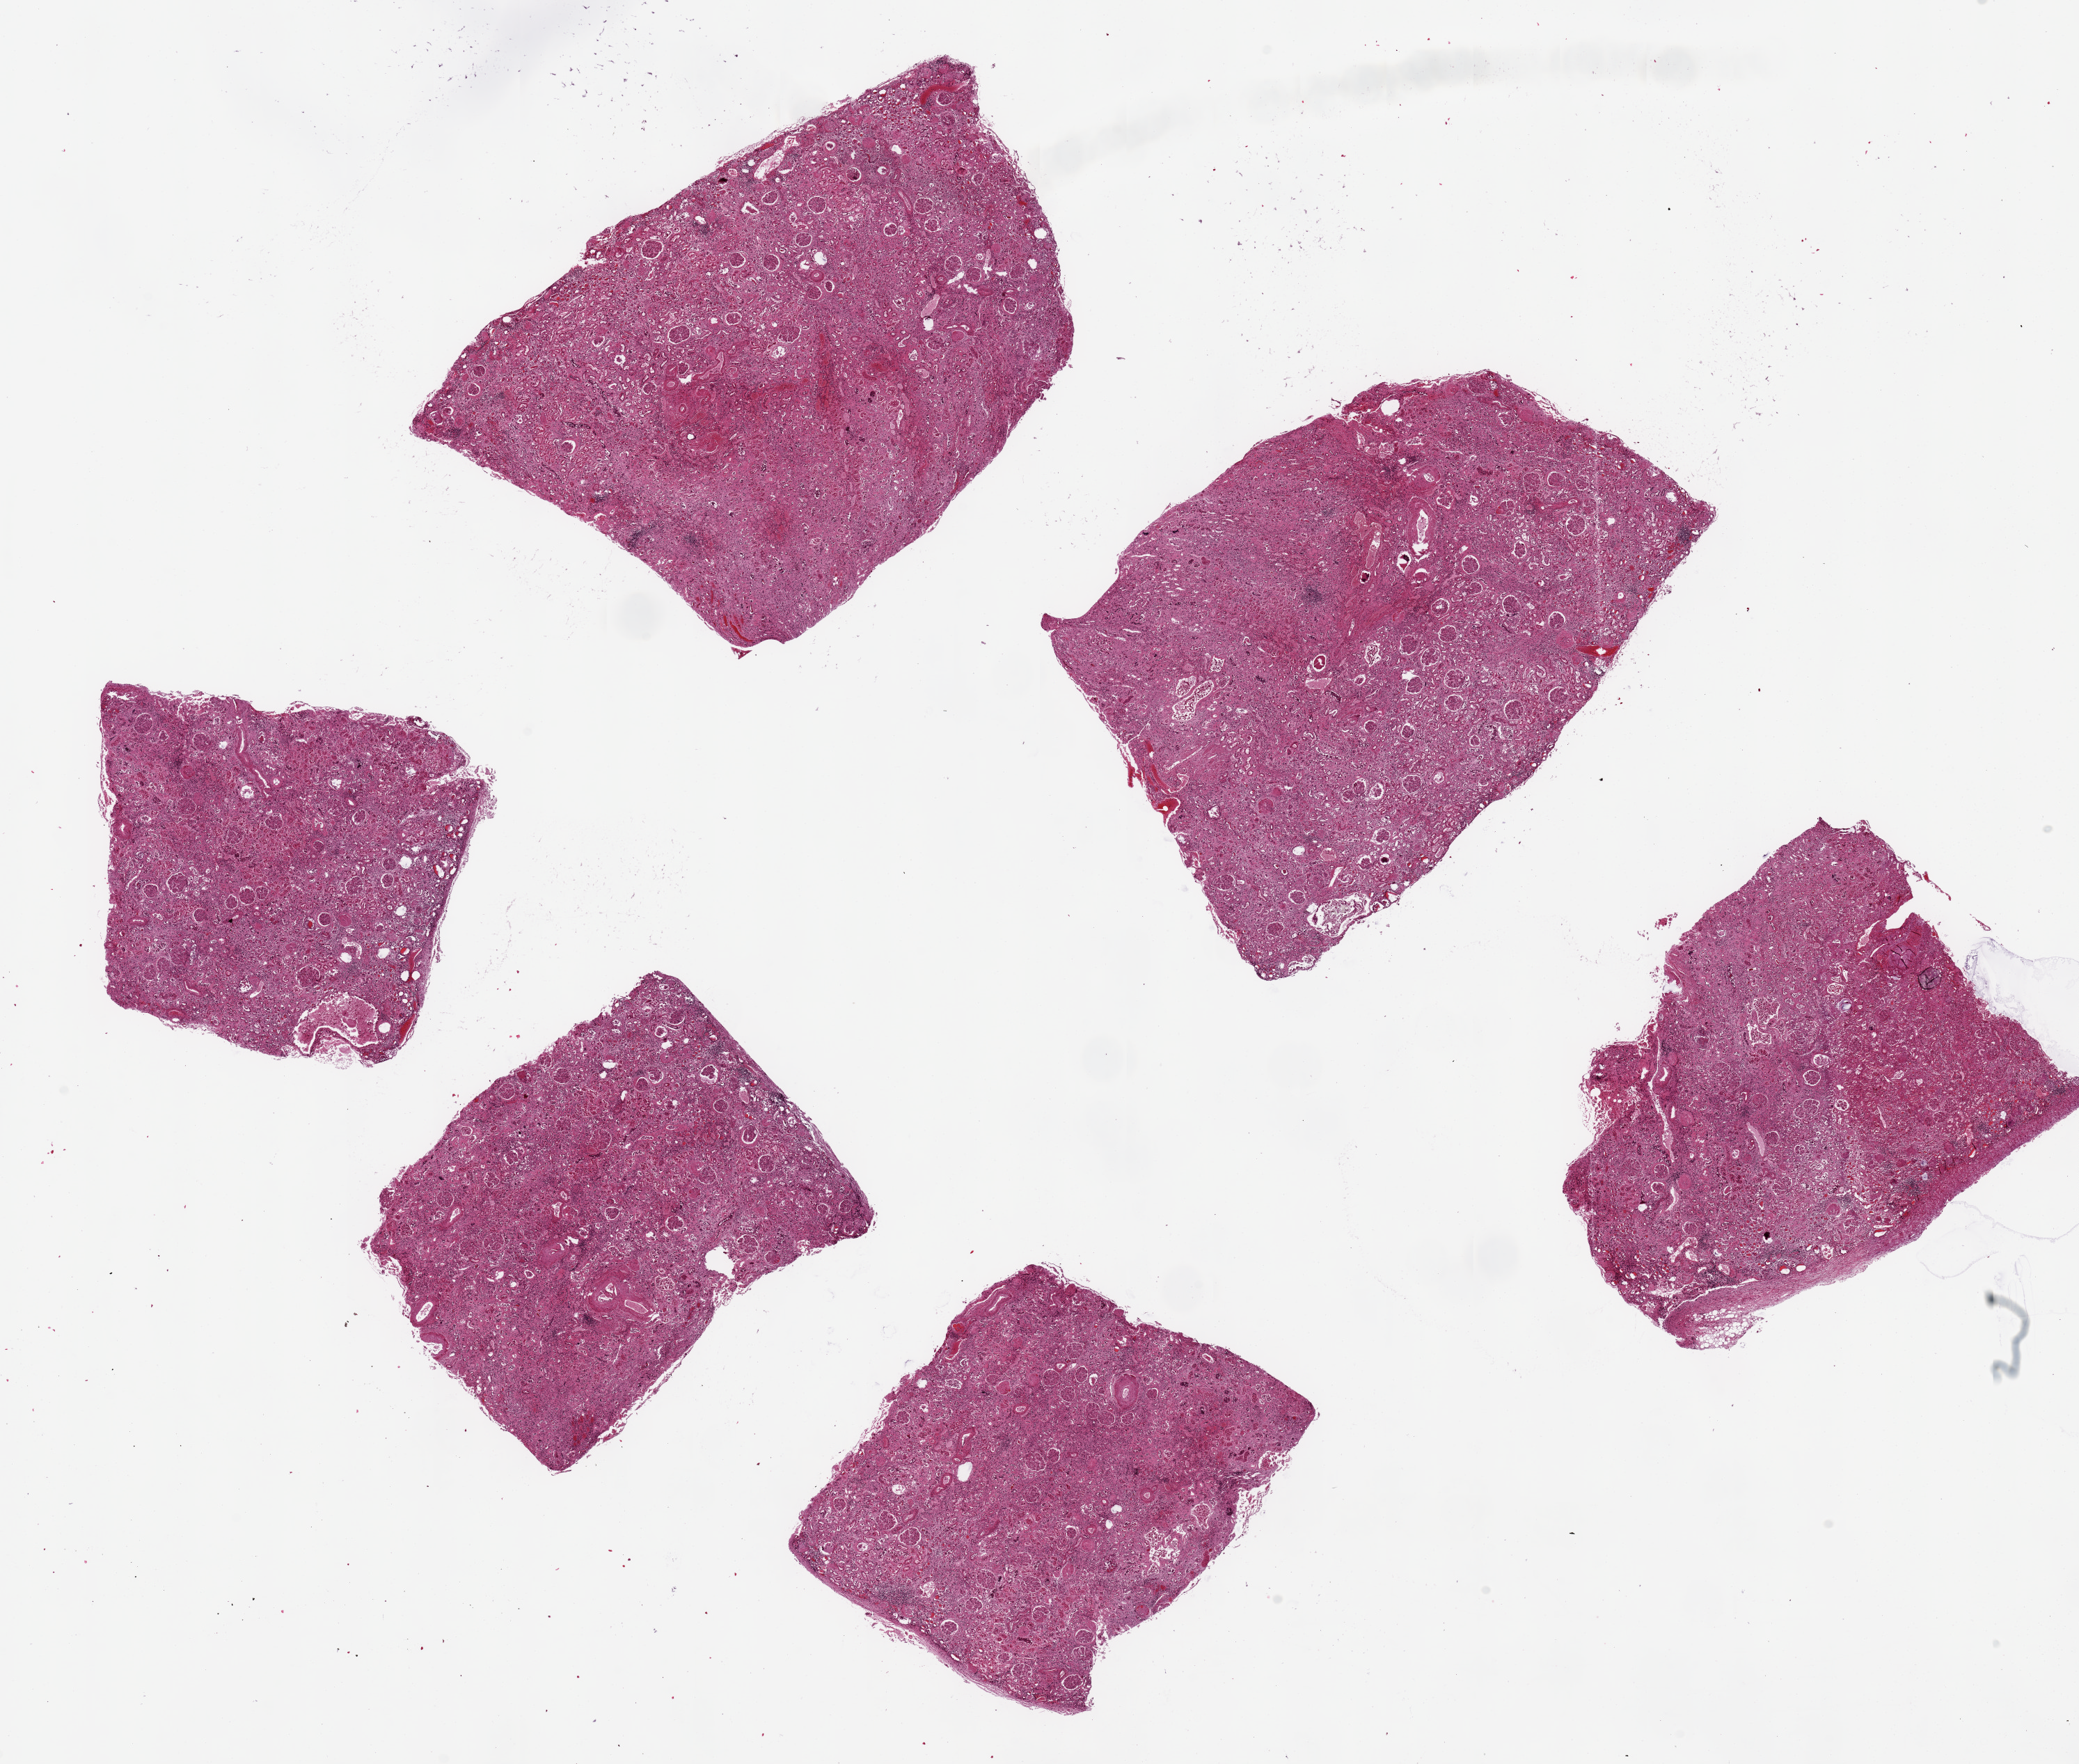
H&E whole-slide image, shown as a low-resolution overview of the whole scanned area (about 23.6 x 20.0 mm, acquisition: 20x scan). PAXgene-fixed paraffin-embedded (PFPE) section. Target tissue: renal cortex. Tissue donor sample. Donor sex: female.
Reviewer comment on this tissue sample: 6 ~6x5mm pieces. Chronic interstitial nepthritis. Both glomeruli and tubules show severe autolysis.